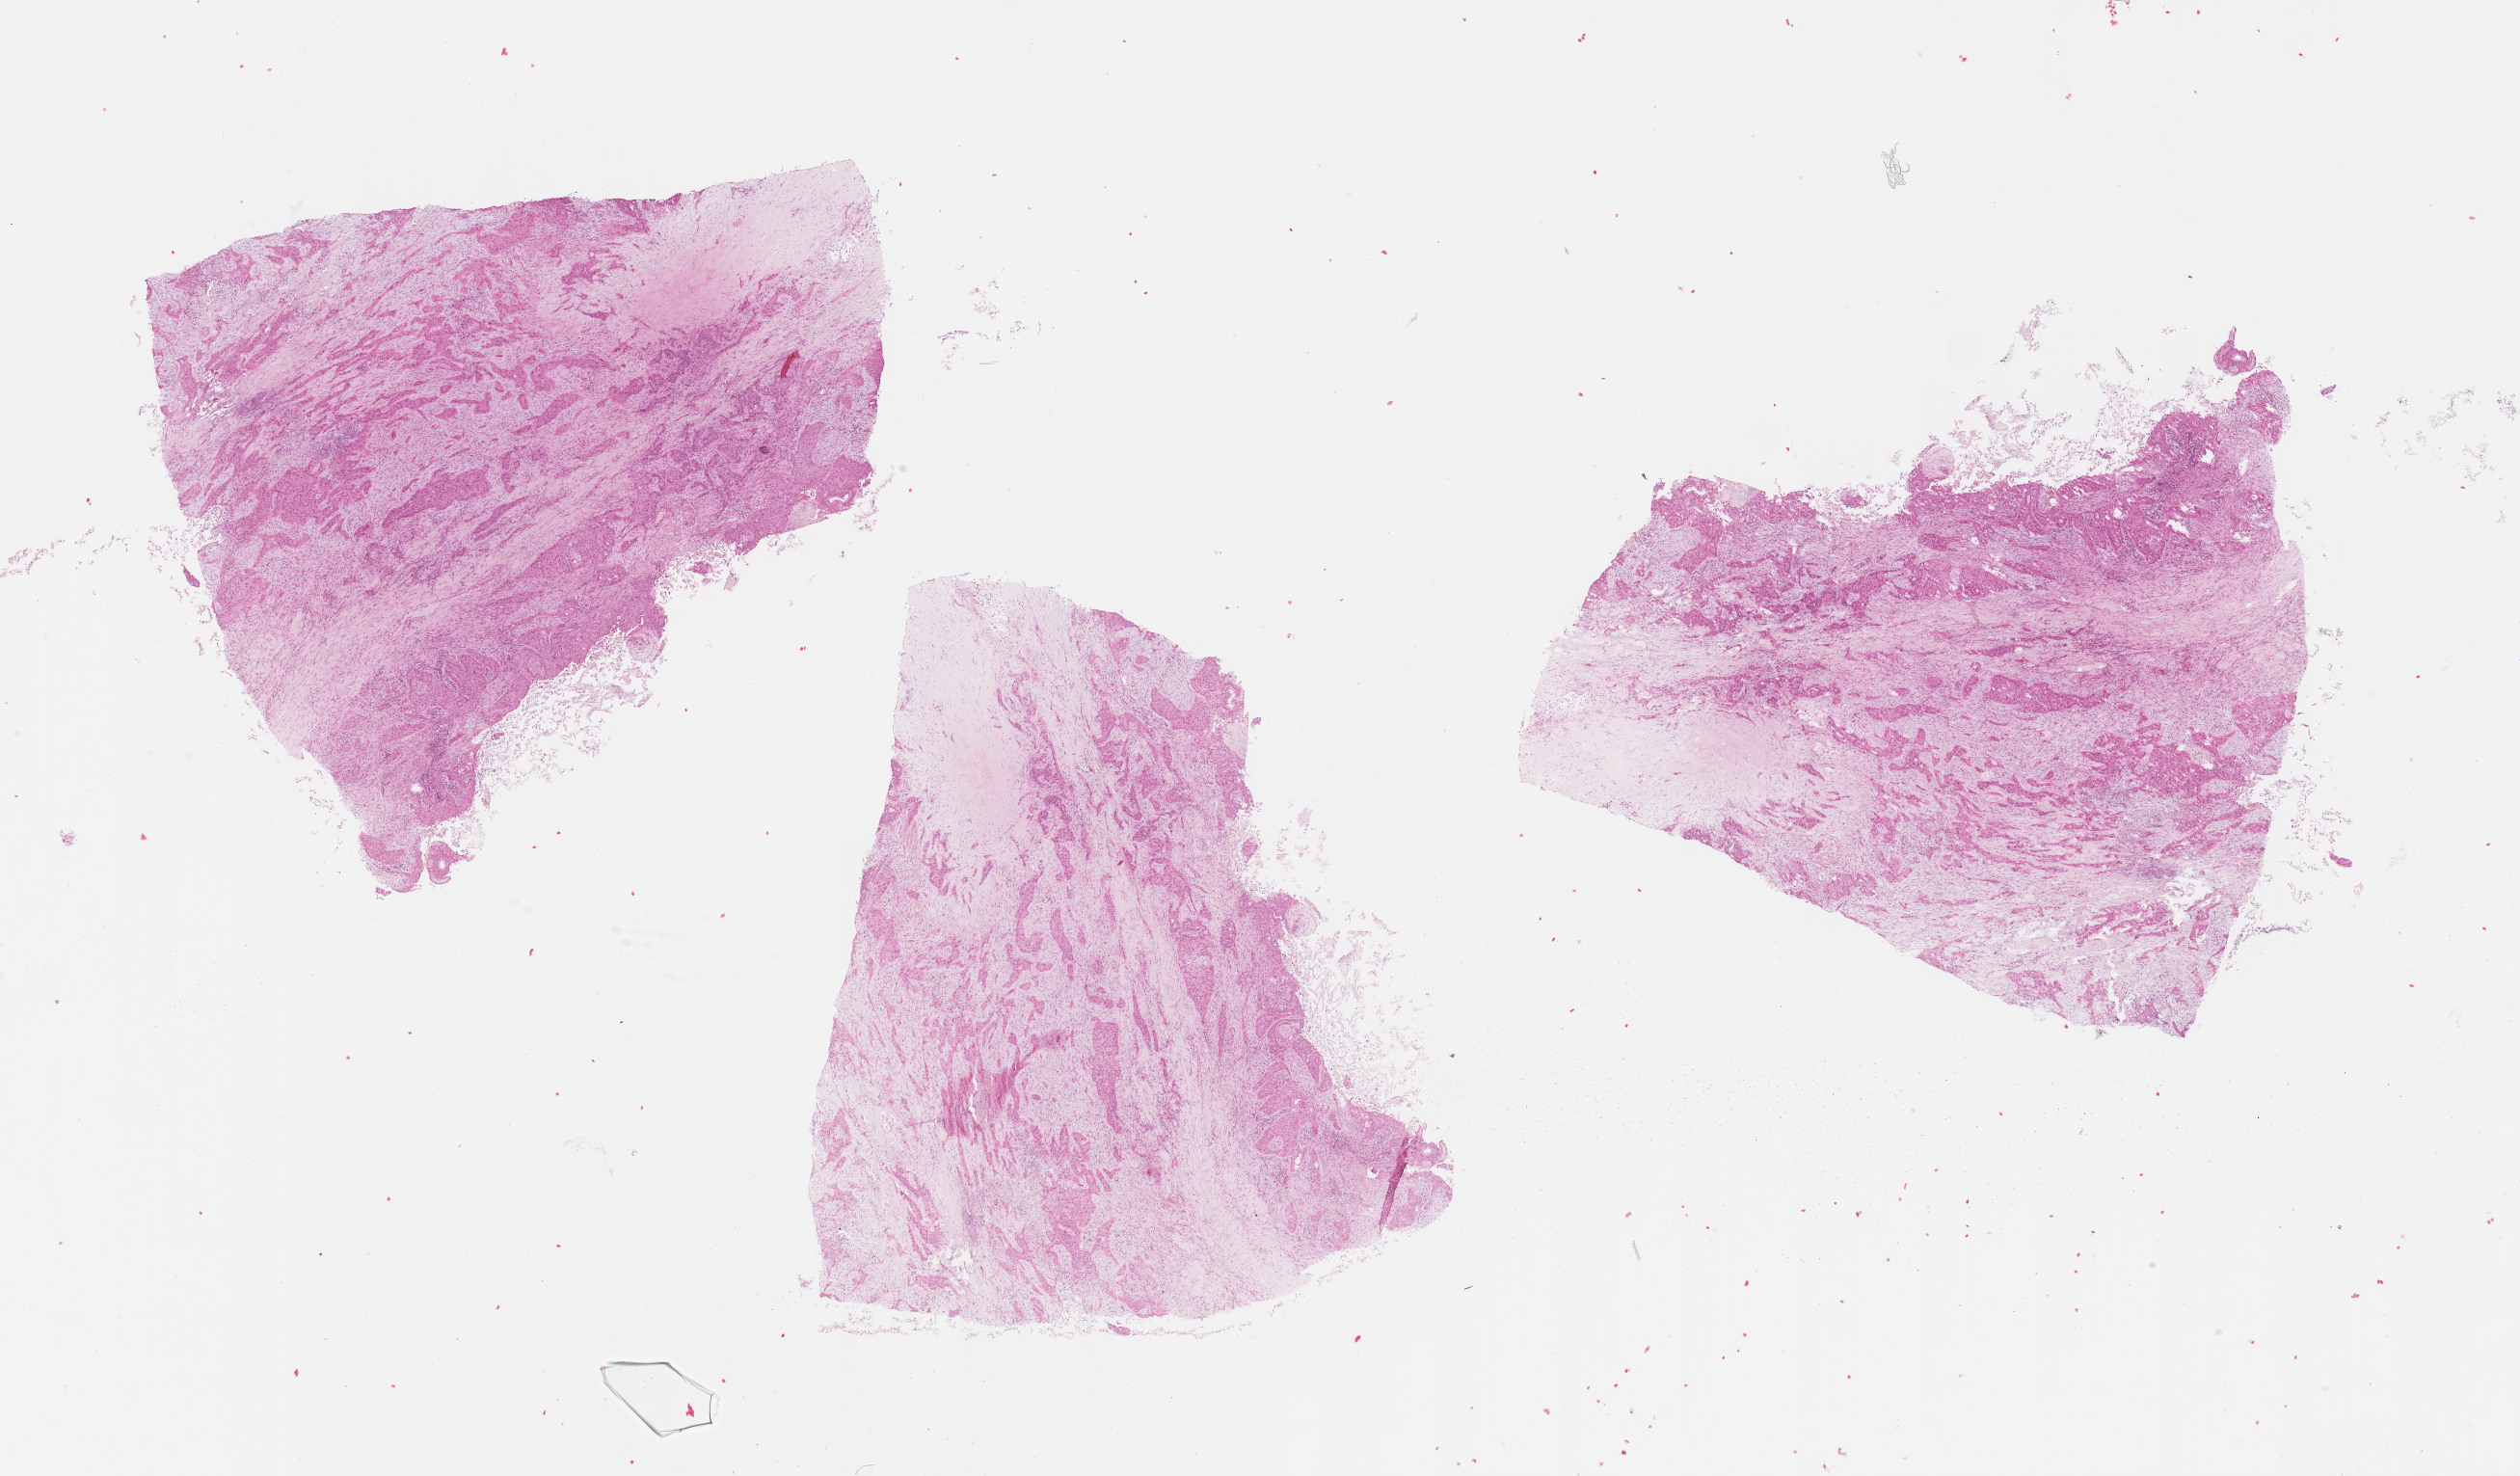
Whole-slide histology image, H&E-stained — a low-resolution overview of the entire scanned area, about 21.0 x 12.3 mm (slide scanned at 20x); lung, tumour tissue. Patient: female, age 66 years.
• patient diagnosis (cohort enrolment): squamous cell carcinoma (lung)